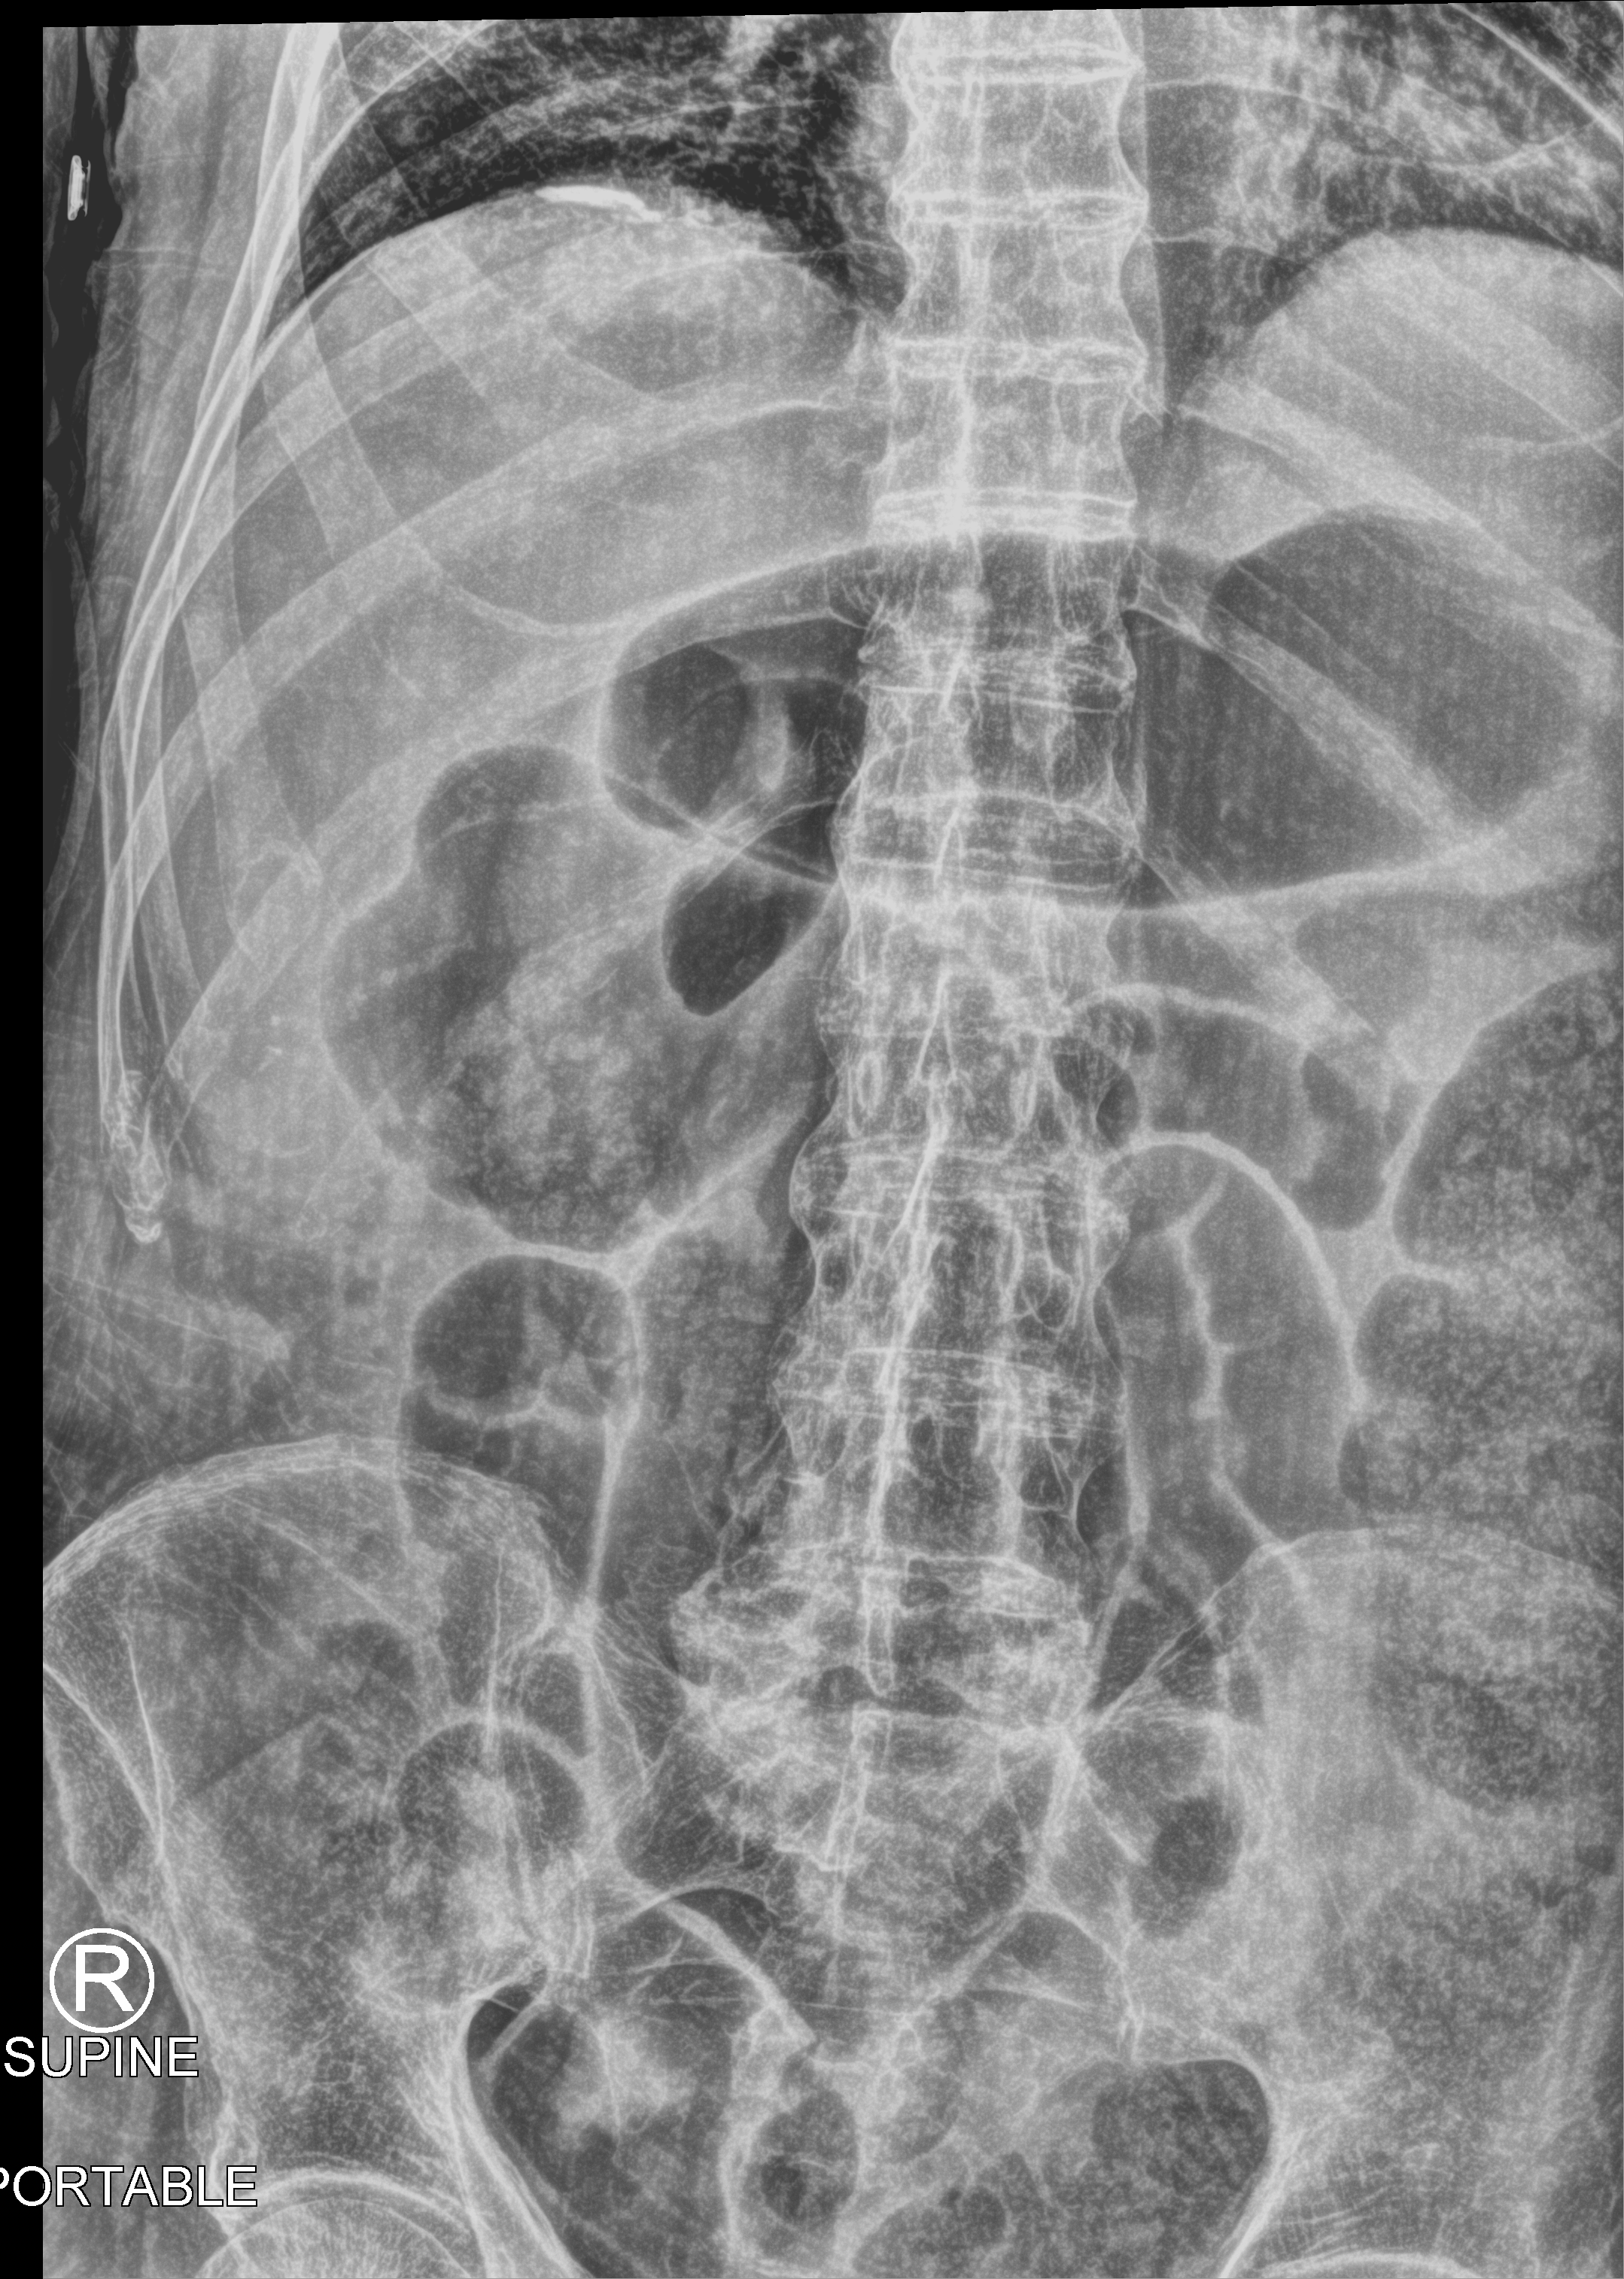
Portable abdomen radiograph. Male patient hospitalised with COVID-19, age 75–90 years.
From the hospital-stay record, not from the radiograph (when in the stay this image was taken is not recorded): mechanically ventilated during this hospital stay: no; admitted to intensive care during this hospital stay: no; length of hospital stay: 1 day.